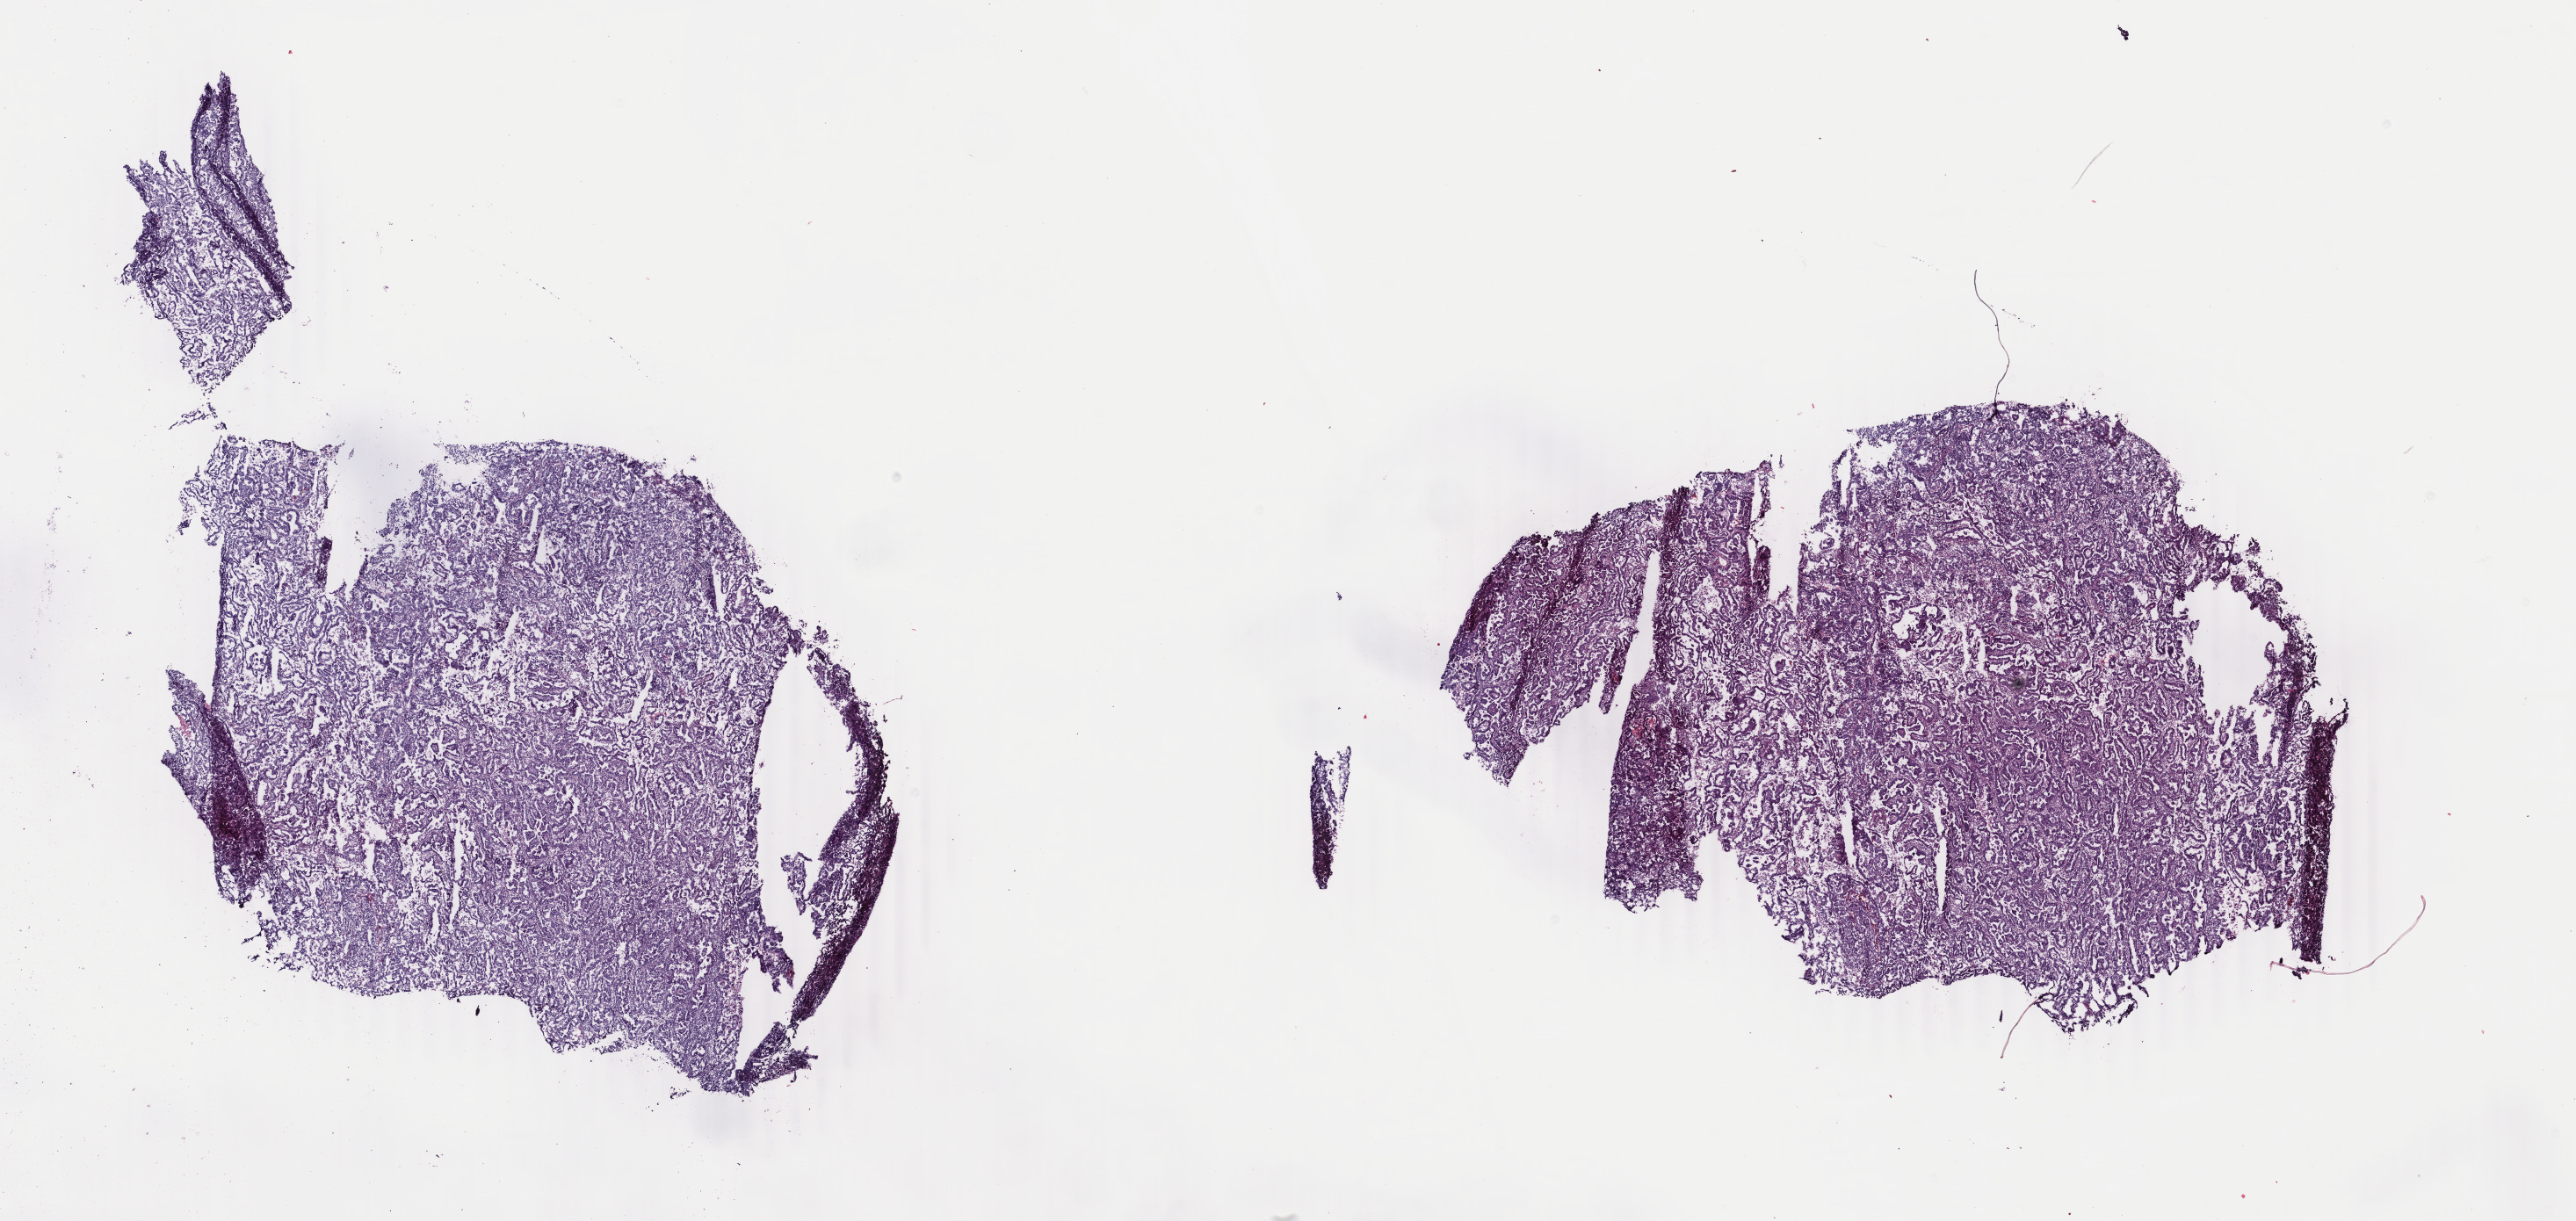
H&E-stained whole-slide image — low-resolution overview of the scanned area, about 23.3 x 11.1 mm (from a 40x scan). Frozen section. Primary tumour sample from the uterus. Patient: female, age at initial diagnosis 79 years. Histologic grade: G3 (poorly differentiated). Composition of this section per pathologist review: tumour cells 45%, tumour nuclei 60%, normal cells 0%, stromal cells 45%, necrosis 10%. Inflammatory infiltration, as recorded: lymphocyte infiltration 10%, monocyte infiltration 4%, neutrophil infiltration 2%.
Pathologic diagnosis: Serous cystadenocarcinoma, NOS (endometrium). FIGO stage: IIIC.